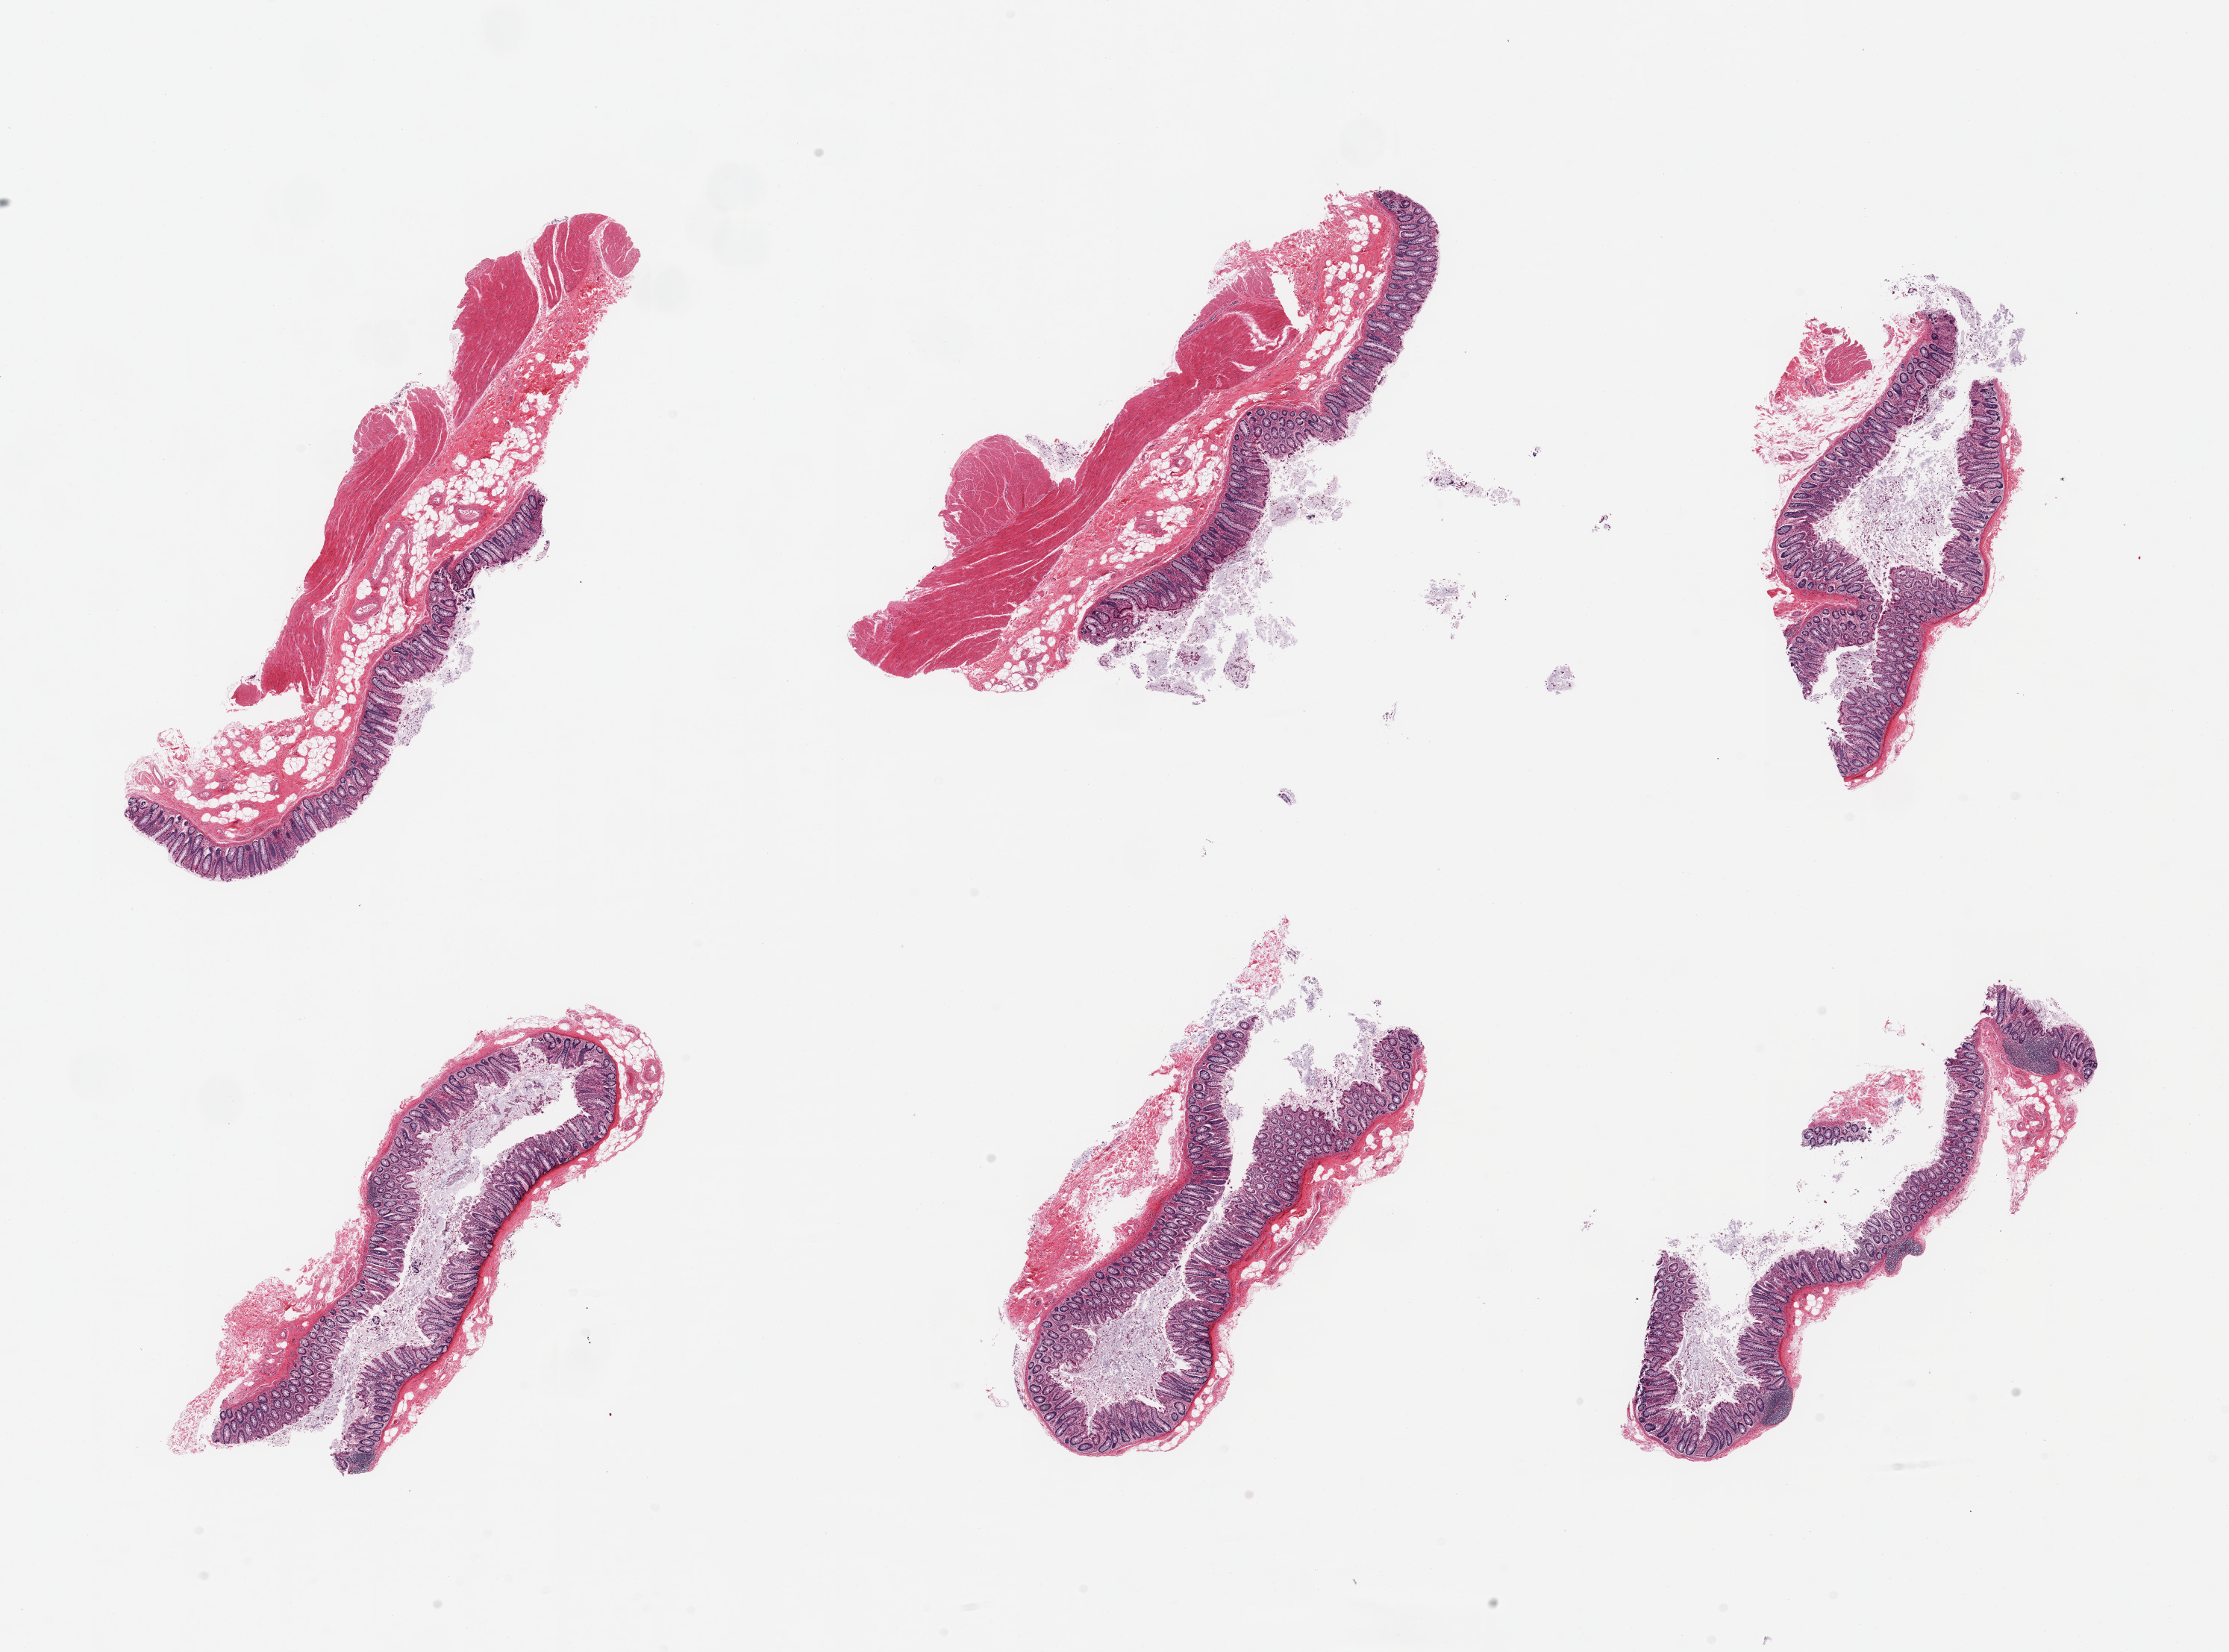
Whole-slide image, H&E stain, brightfield — a low-resolution overview of the entire scanned area, about 23.6 x 17.5 mm (acquisition: 20x scan); PAXgene-fixed paraffin-embedded (PFPE) section; section of transverse colon (target tissue); tissue donor sample.
Pathologist's review note for this sample: 6 pieces; only 2 have full thickness; 4 have mucosa only.